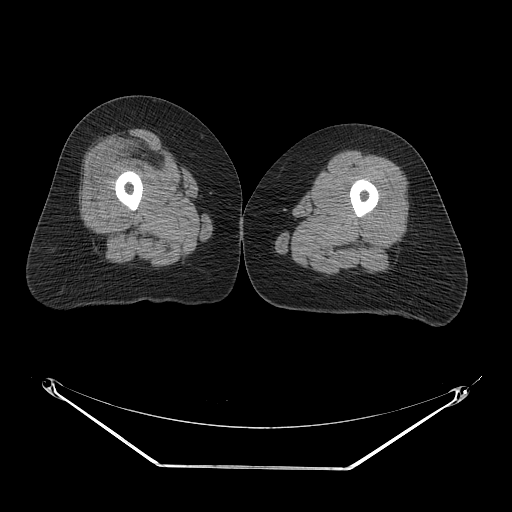
CT of an extremity soft-tissue mass (from a PET/CT study), one axial slice. Position 20 of 267 along the scan axis. Soft-tissue window (W 400 / L 40 HU). 512 × 512 image matrix, field of view 500 × 500 mm. Female patient. Case-level facts recorded for this patient, not image findings: histological type: malignant solitary fibrous tumor; grade: intermediate; site of the primary tumour: right thigh.
Outlined on this slice (expert contour drawn on MRI and transferred to this co-registered scan by the dataset authors):
- gross tumour volume including surrounding oedema: bounding box <121,130,186,177> (left, top, right, bottom; pixels)